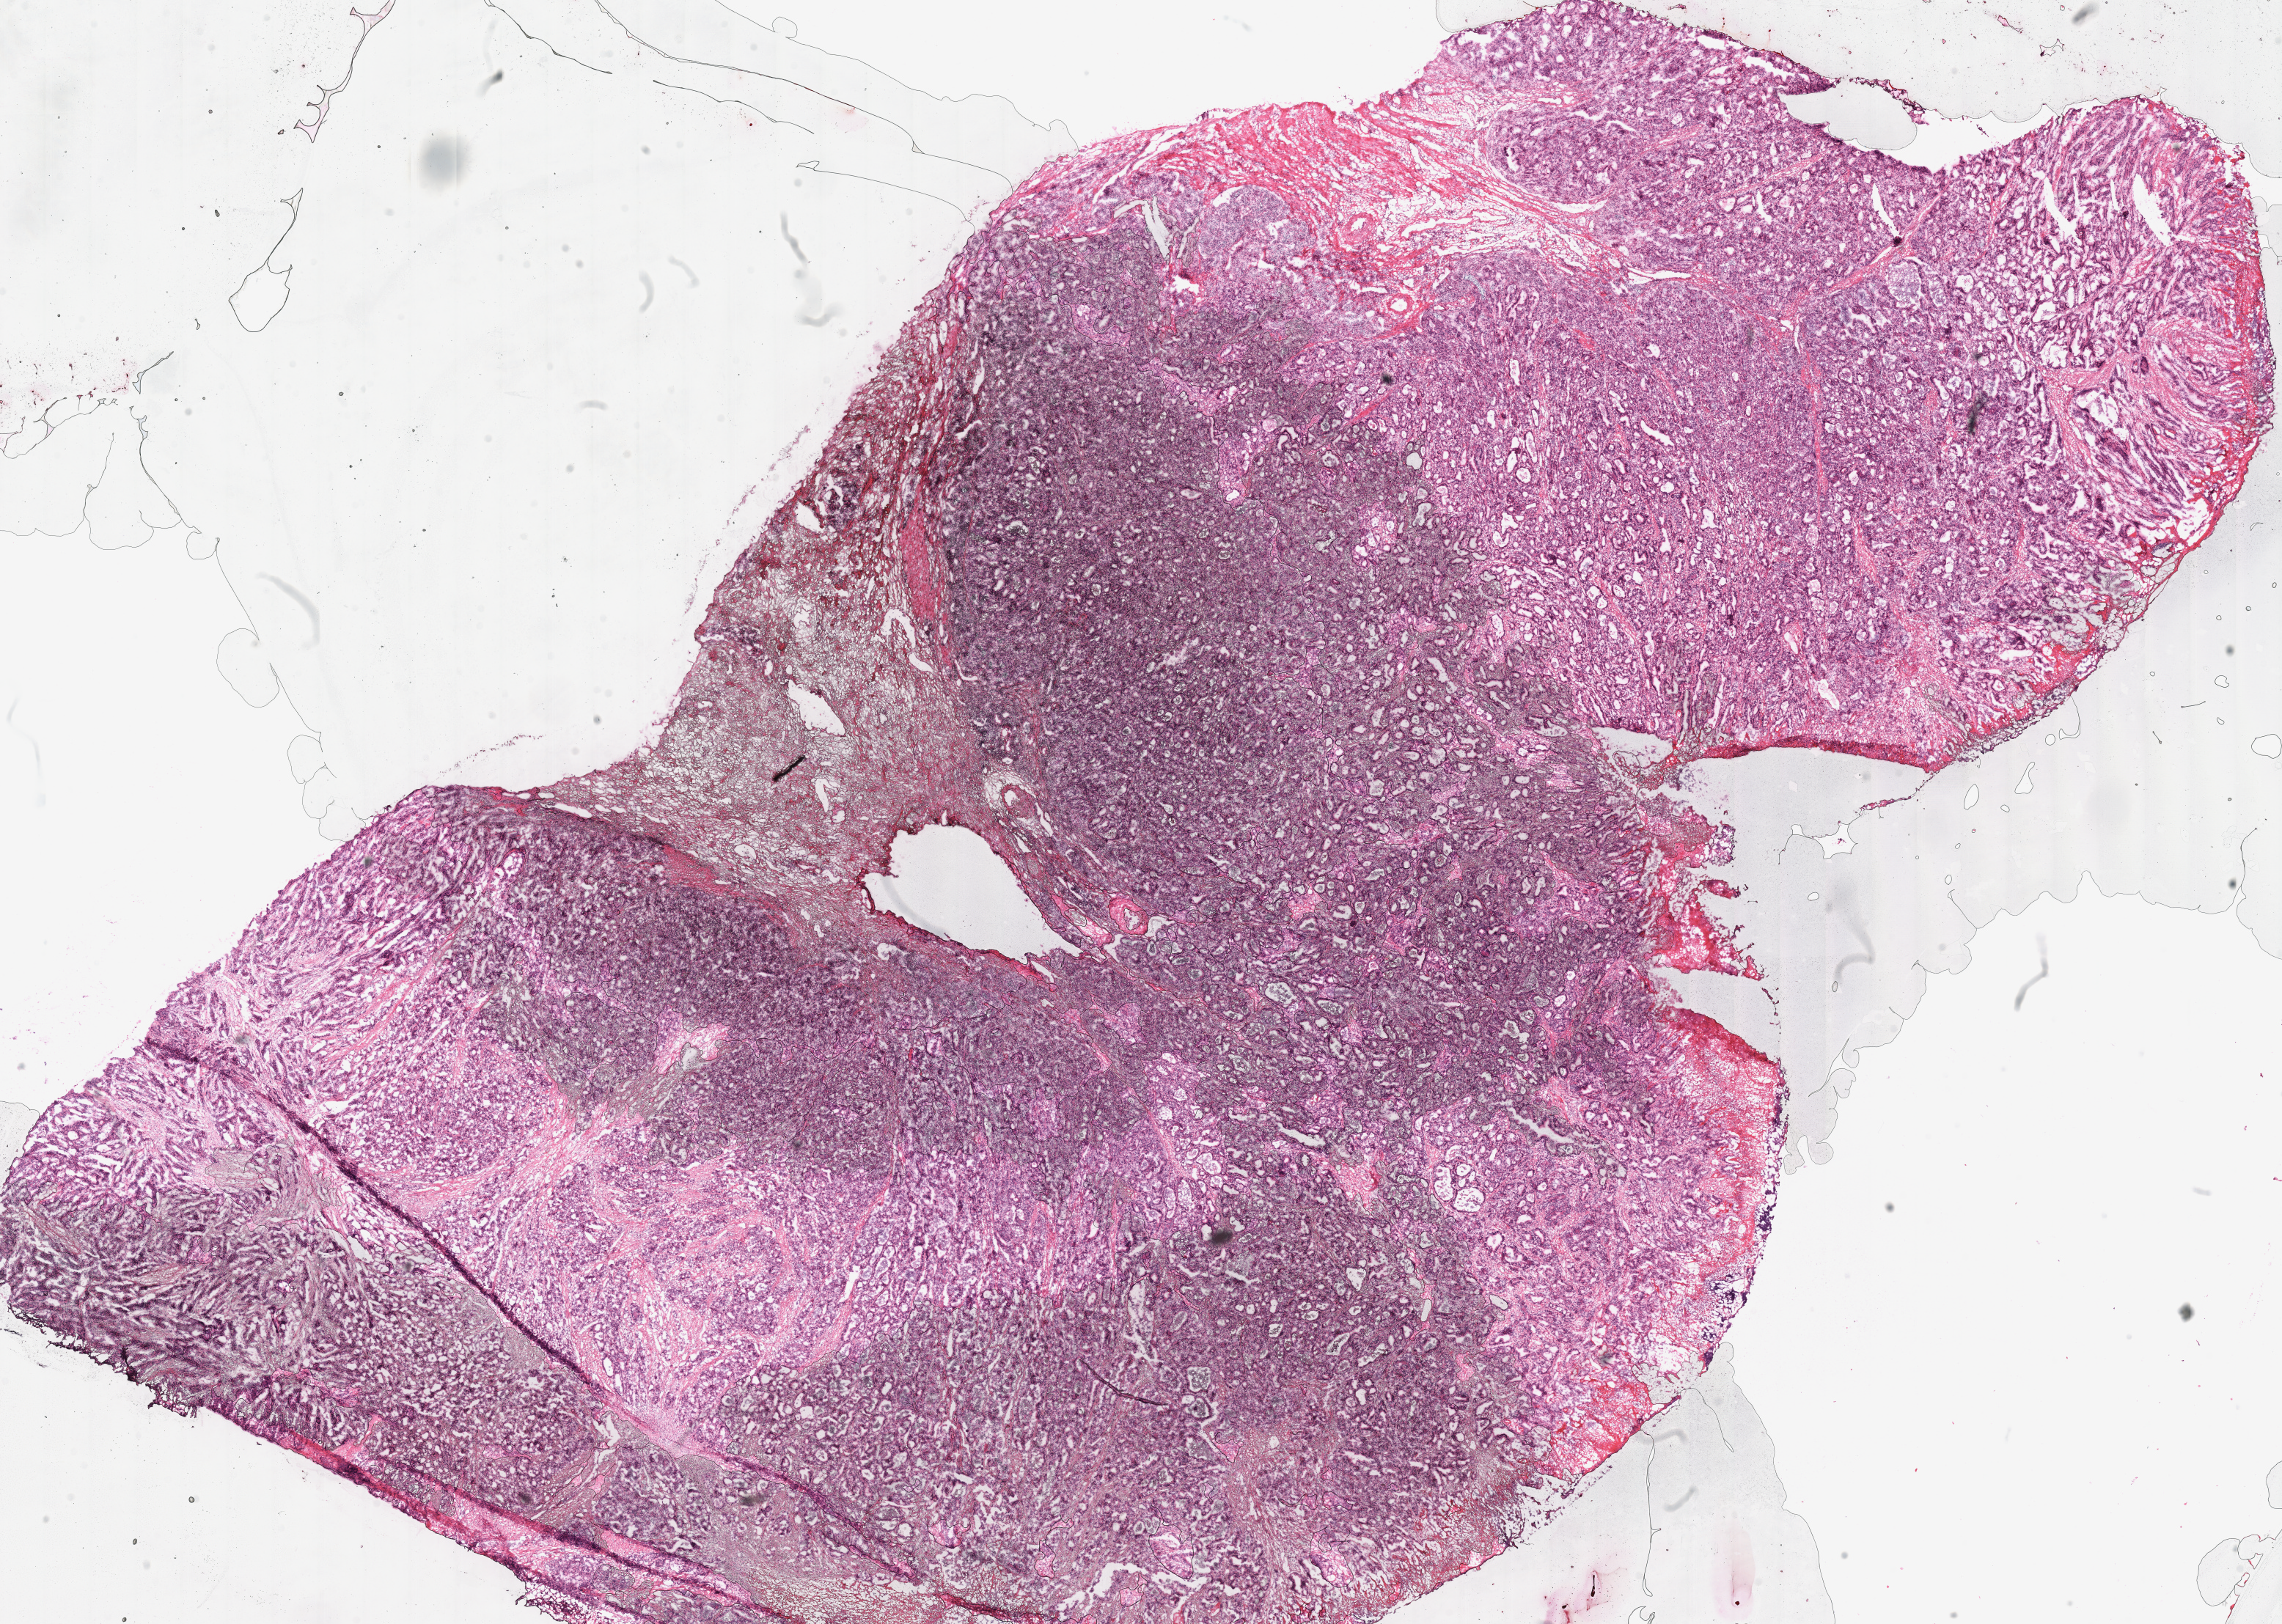
H&E whole-slide image — shown as a low-resolution overview of the whole scanned area (about 24.5 x 17.4 mm); frozen section from the top of the tissue portion; stomach, primary tumour sample. Male, age 66 years at initial diagnosis. Histologic grade: G2 (moderately differentiated). Composition of this section per pathologist review: tumour cells 85%, tumour nuclei 80%, normal cells 0%, stromal cells 15%, necrosis 0%.
* AJCC pathologic stage: IIA (7th edition)
* lymph nodes positive (case pathology): 0 of 15 examined
* diagnosis: Adenocarcinoma, intestinal type